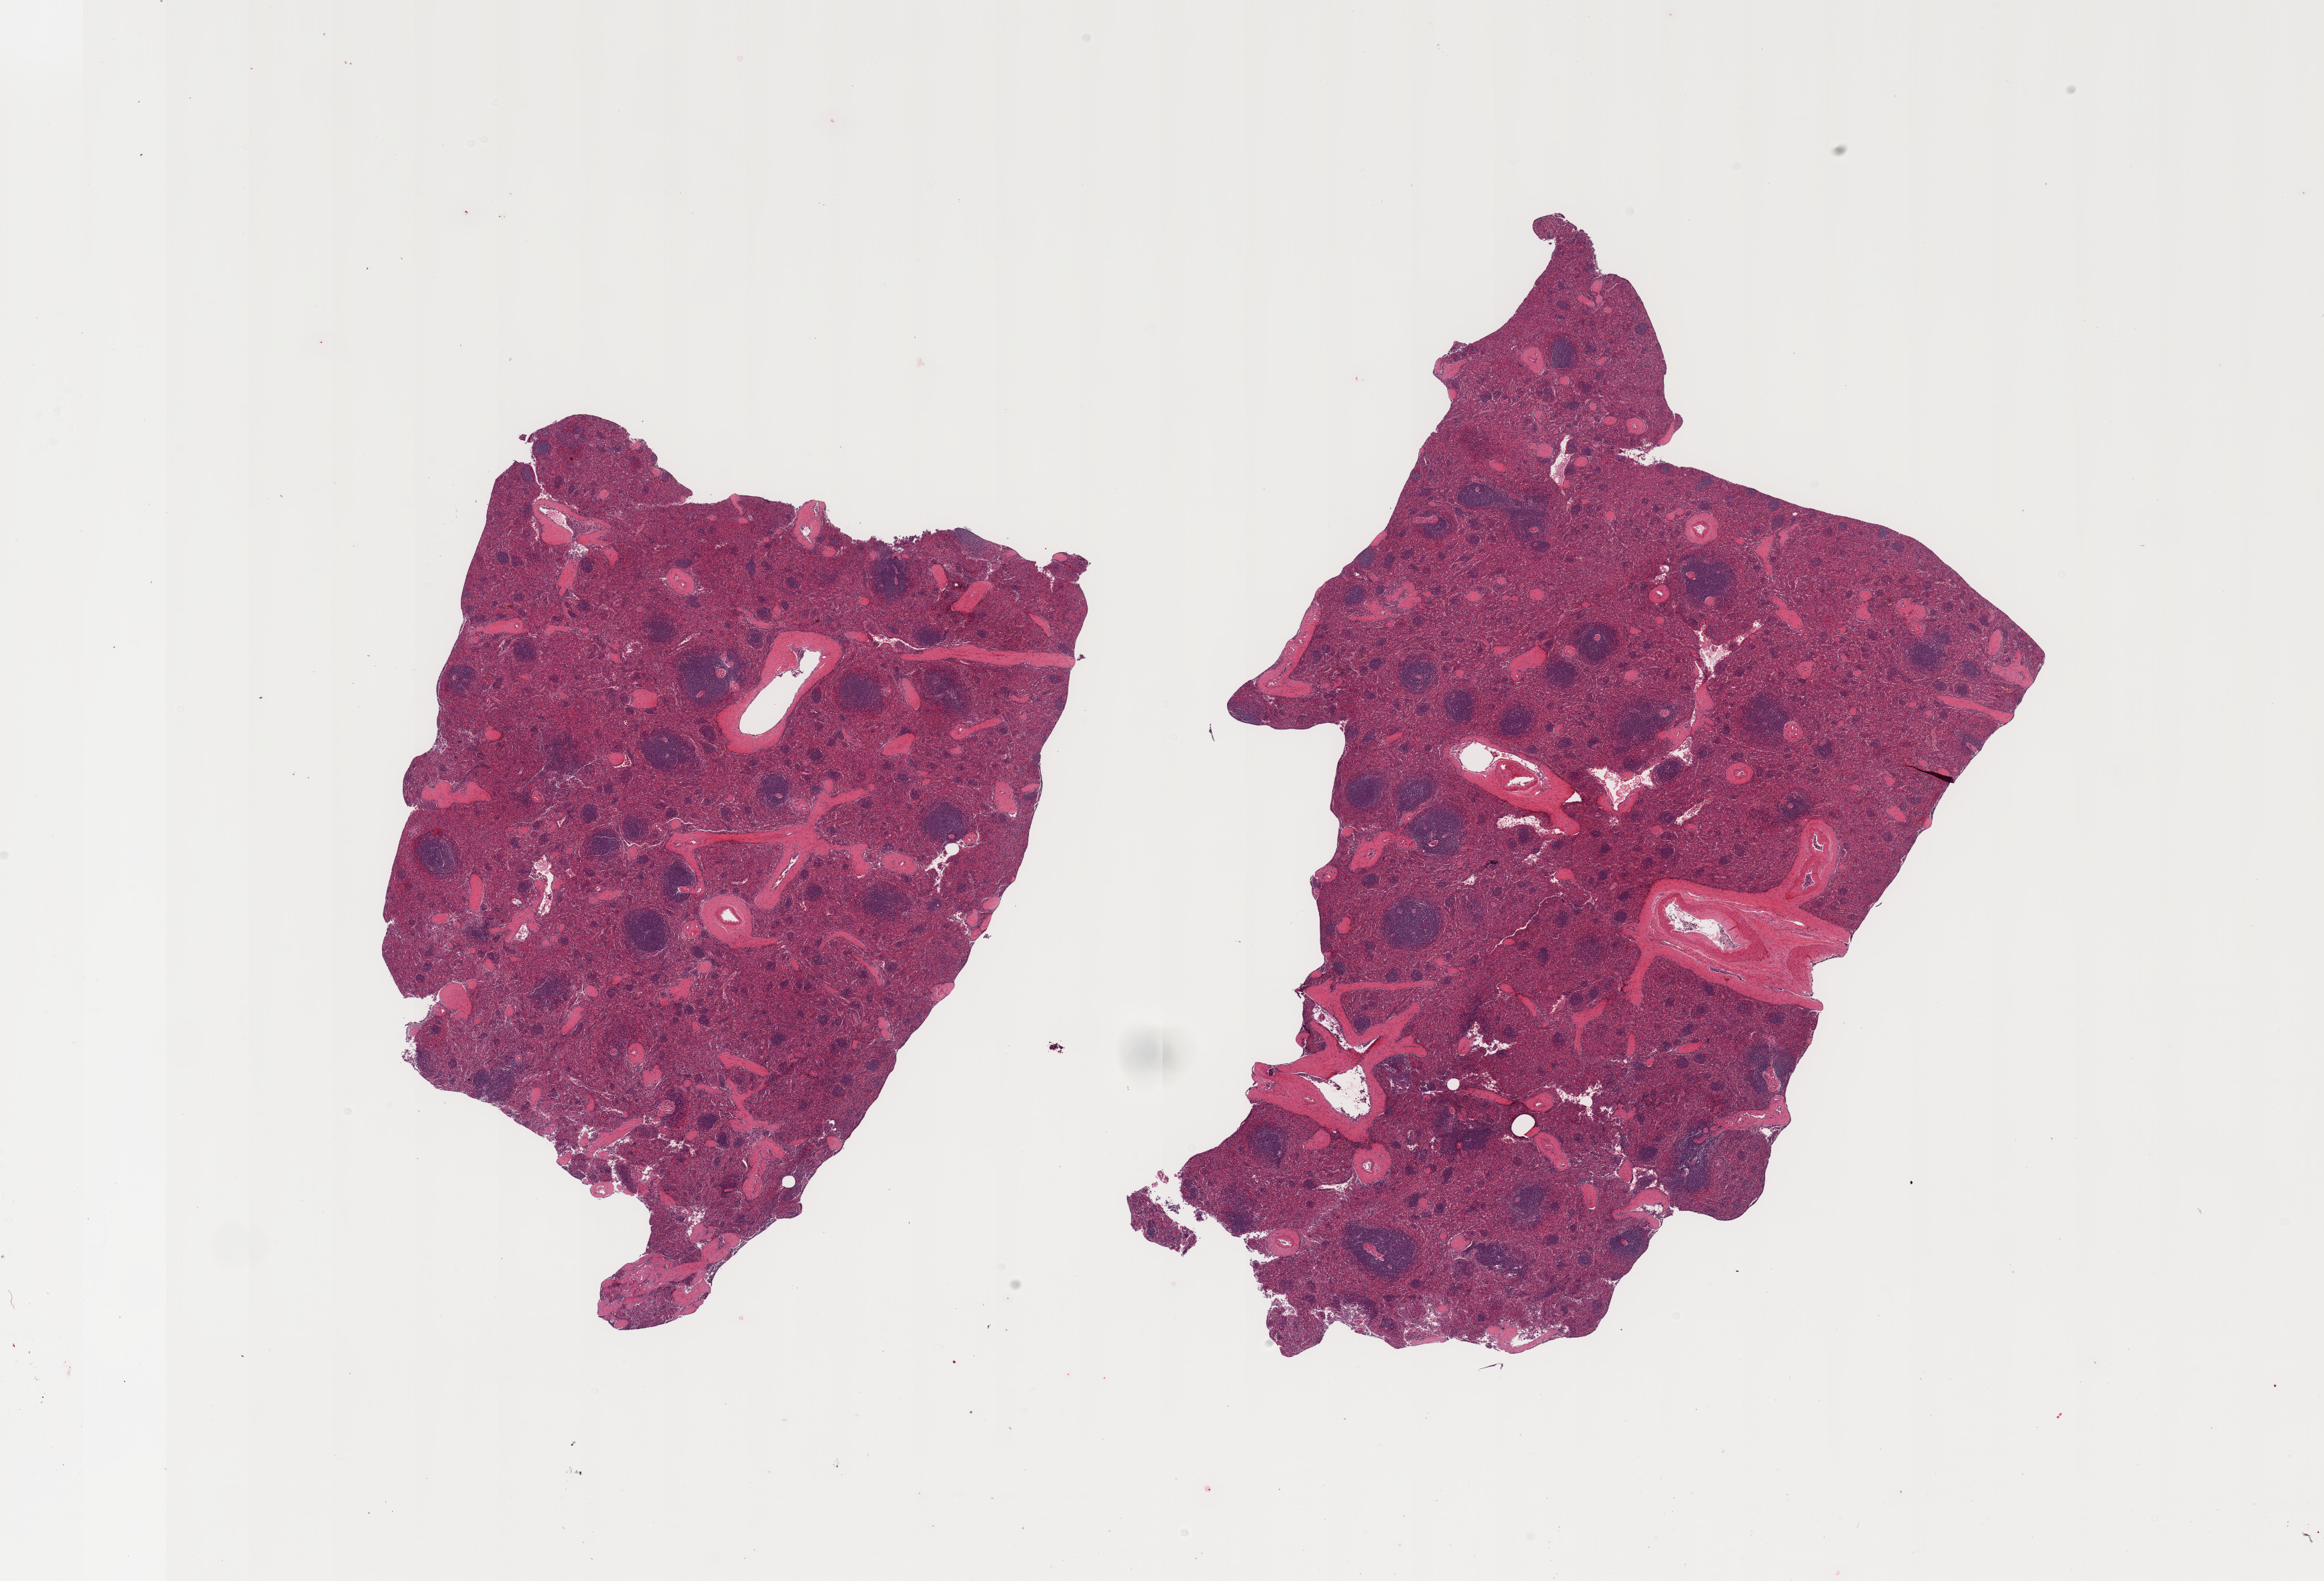
Whole-slide image, H&E stain, a low-resolution overview of the entire scanned area, about 27.6 x 18.8 mm; PAXgene-fixed, paraffin-embedded tissue; target tissue: spleen; donor tissue sample.
* pathologist's review note for this sample: 2 pieces